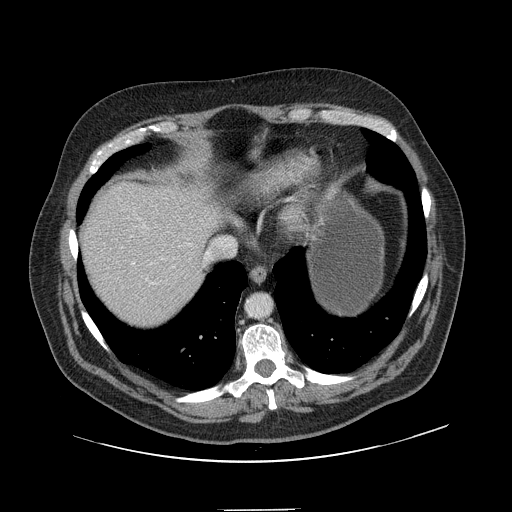
Contrast-enhanced abdominal CT, one axial slice. Position 130 of 154 along the scan axis. 120 kVp. Intravenous contrast given. Soft-tissue window (W 400 / L 40 HU). 2.5 mm slice thickness. 512 × 512 image matrix. Male patient, age 61 years. From the clinical record (not read from this slice): diagnosis: colorectal cancer liver metastases, imaged before liver resection; multiple liver metastases: yes; largest metastasis: 2.6 cm; disease in both lobes: yes.
Outlined on this slice (manually delineated by an expert):
- hepatic veins: bounding box (x1, y1, x2, y2) in pixels: (162, 254, 207, 260)
- liver: (81, 184, 219, 327)
- planned liver remnant (the part of the liver to remain after resection): (81, 183, 220, 326)
- portal vein (with intrahepatic branches): (127, 216, 147, 281)